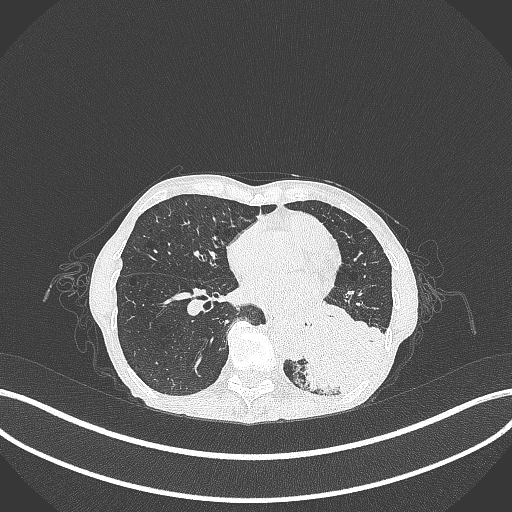
Chest CT, one axial slice. Slice 104 of 347 in the series (ordered by position). Lung window (W 1500 / L -600 HU). 1 mm slice thickness. 512 × 512 image matrix, field of view 400 × 400 mm. Patient: female, 70 years. Case-level facts recorded for this patient, not image findings: clinical TNM (as recorded): T3 N0 M0.
Structures marked on this image (bounding box drawn by a radiologist):
- lung tumour (recorded histology: small cell carcinoma): box from (x=291, y=306) to (x=385, y=397) px